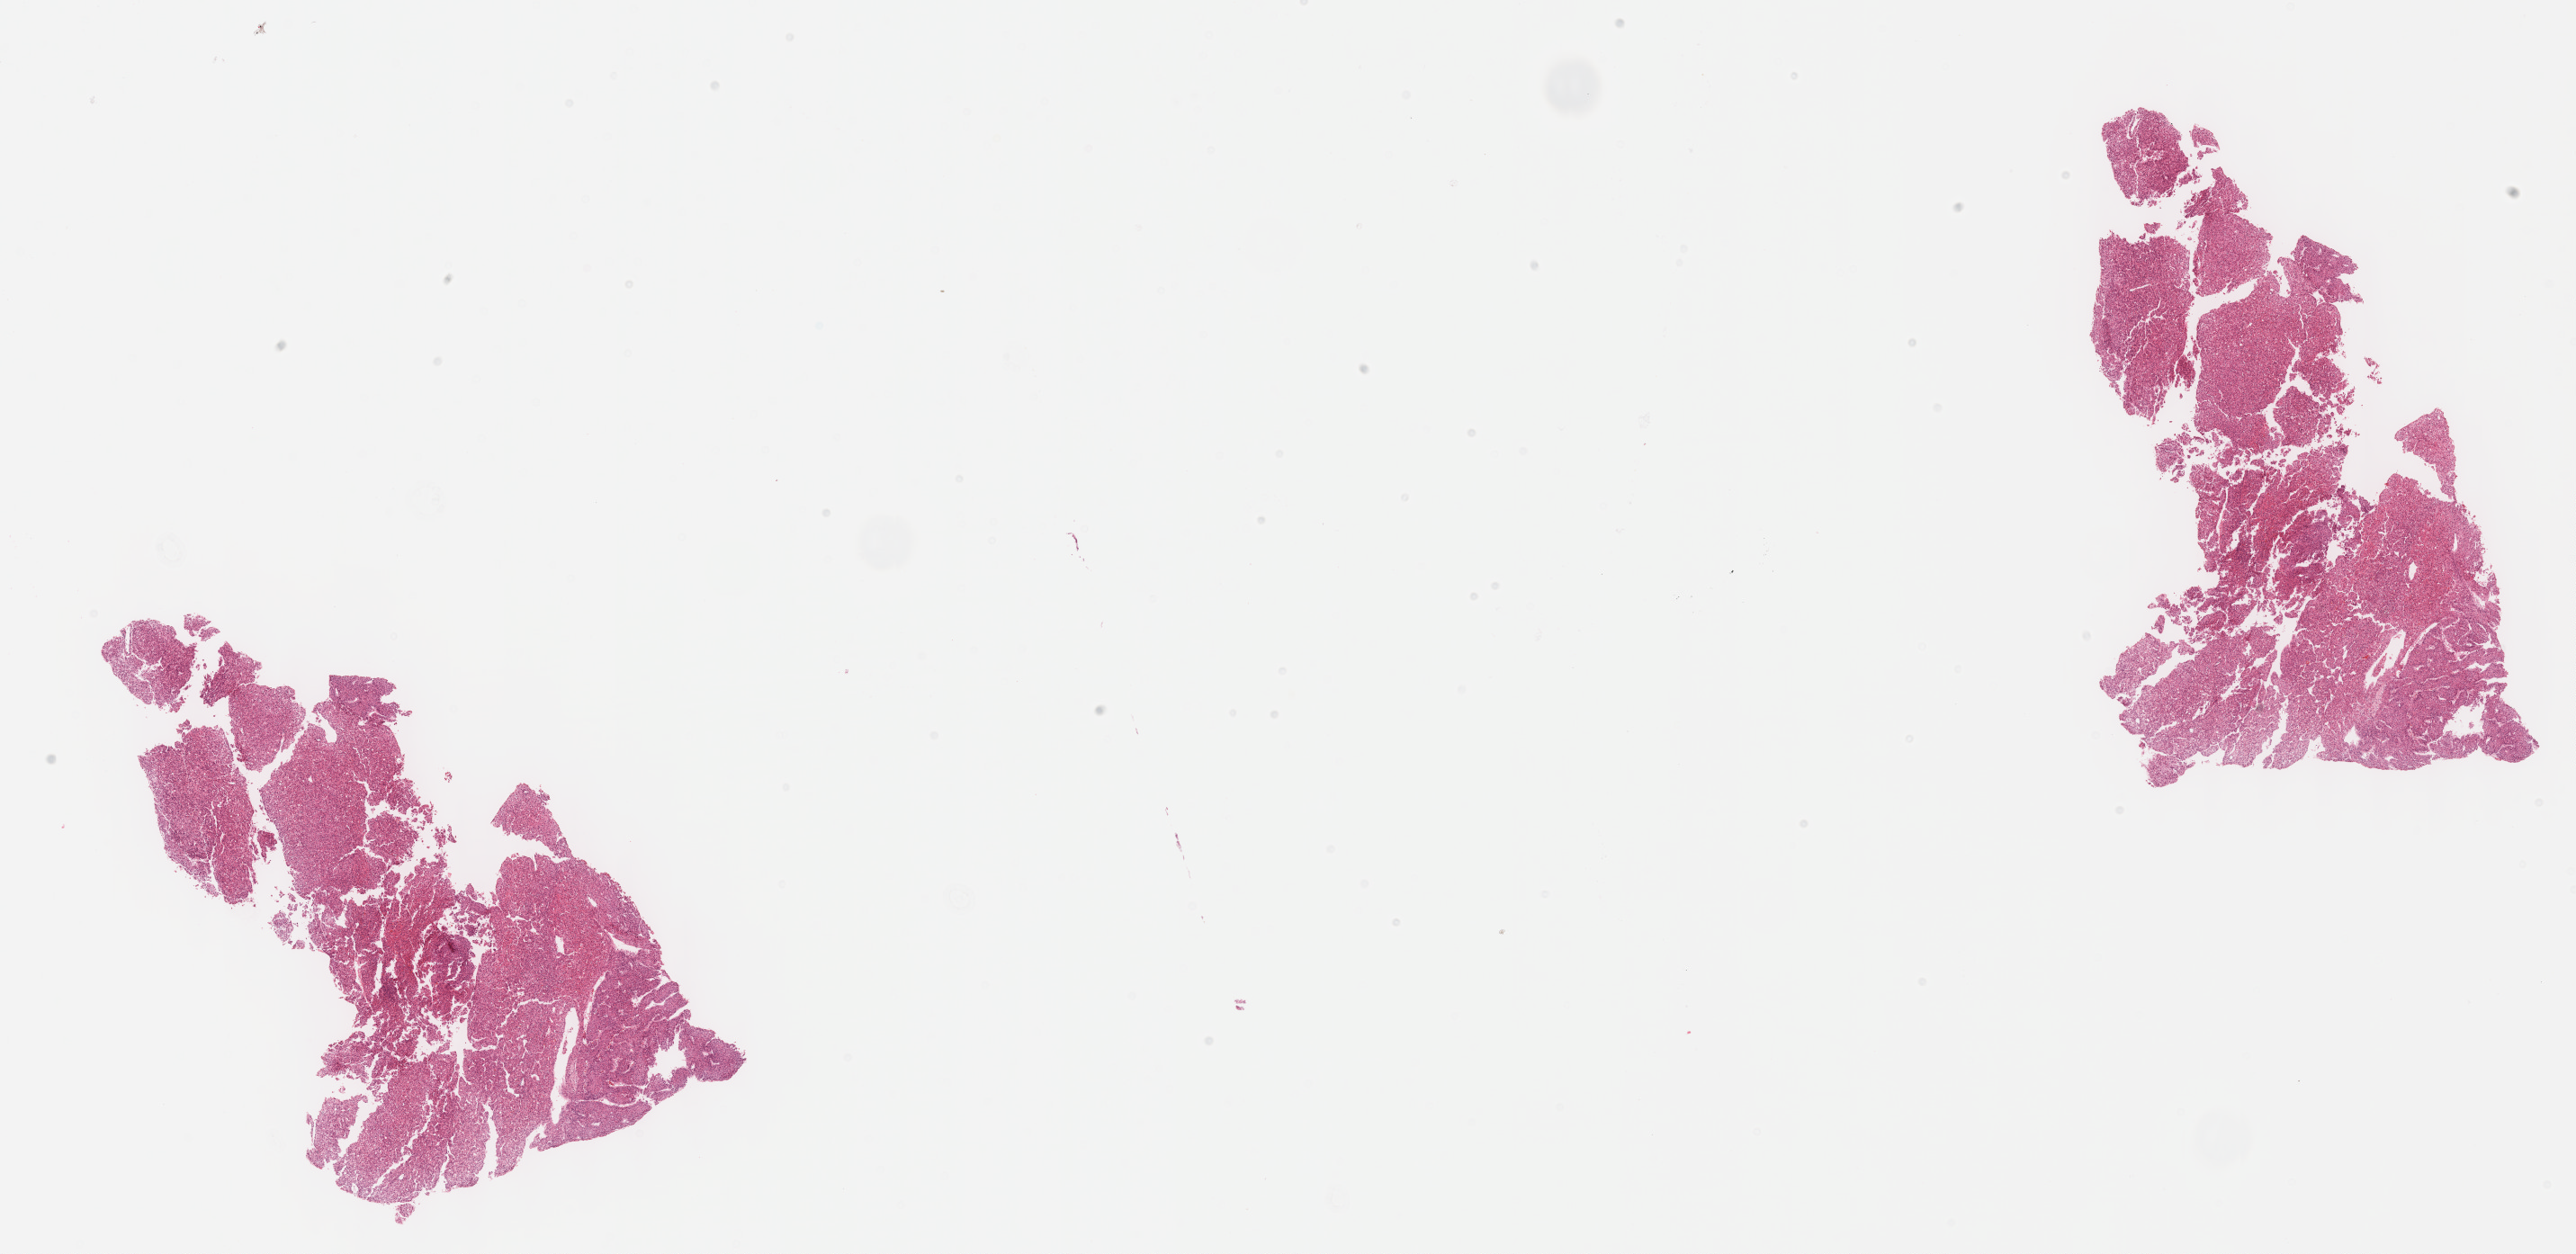
Whole-slide histology image, Hematoxylin and eosin (H&E) stained, whole scanned area (about 23.1 x 11.3 mm, acquisition: 40x scan) shown as a low-resolution overview; formalin-fixed paraffin-embedded (FFPE) diagnostic section; sample: primary tumour, liver. Female patient; age at initial diagnosis 70 years.
Diagnosis: Hepatocellular carcinoma, NOS.